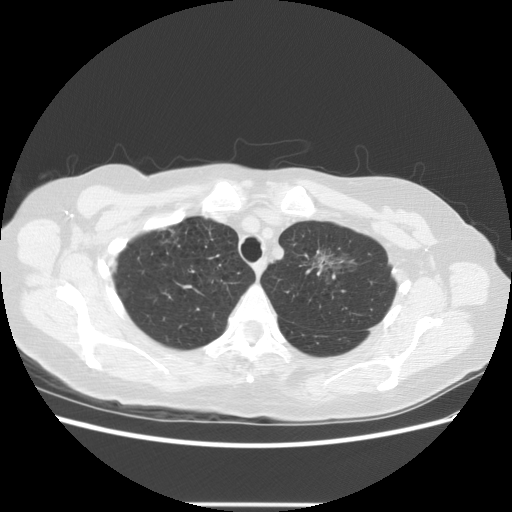
Low-dose screening chest CT, one axial slice. Position 103 of 126 along the scan axis. Lung window (W 1500 / L -600 HU). 2.5 mm slice thickness. 512 × 512 image matrix, field of view 360 × 360 mm.
Structures marked on this image (expert manual segmentation):
- lesion 2 (tumor, upper lobe of left lung): box from (x=316, y=252) to (x=333, y=269) px